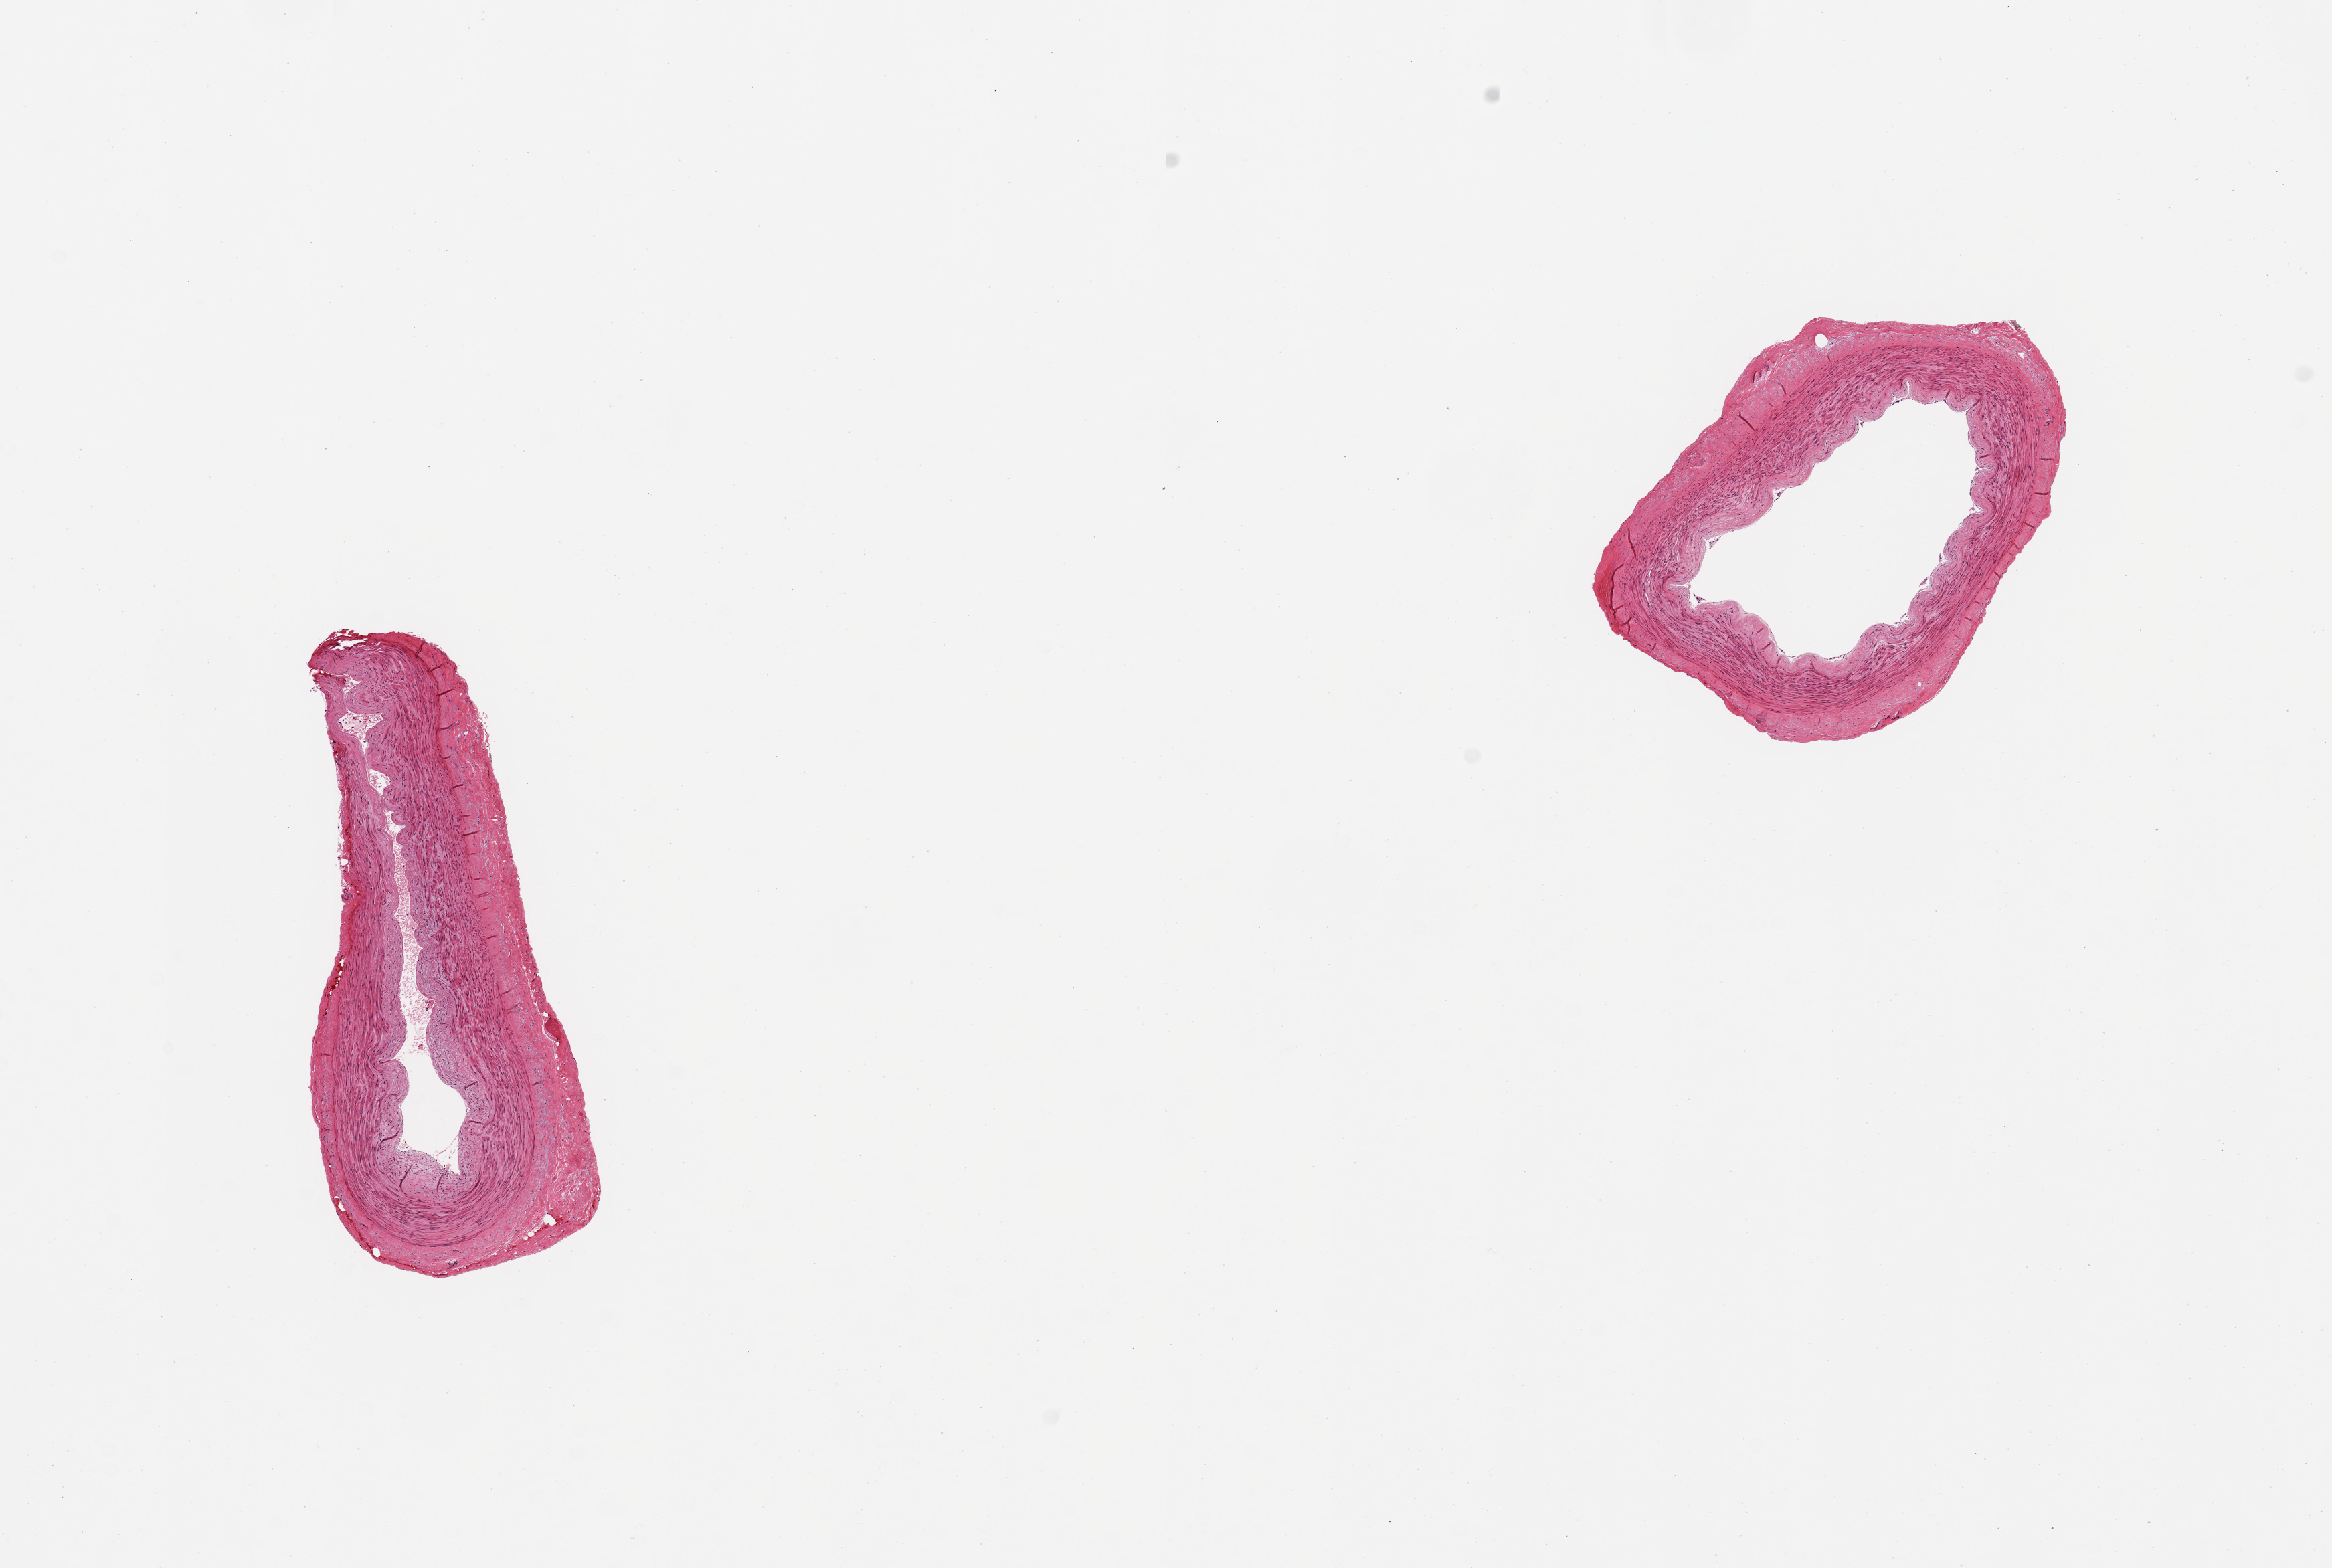
Digitized H&E-stained section, brightfield — shown as a low-resolution overview of the whole scanned area (about 13.8 x 9.3 mm, from a 20x scan); PAXgene-fixed paraffin-embedded (PFPE) section; section of tibial artery (target tissue); tissue donor sample. Donor: male.
Review note (as recorded): 2 pieces; up to 0.3mm rim of adventitia, lumen open.